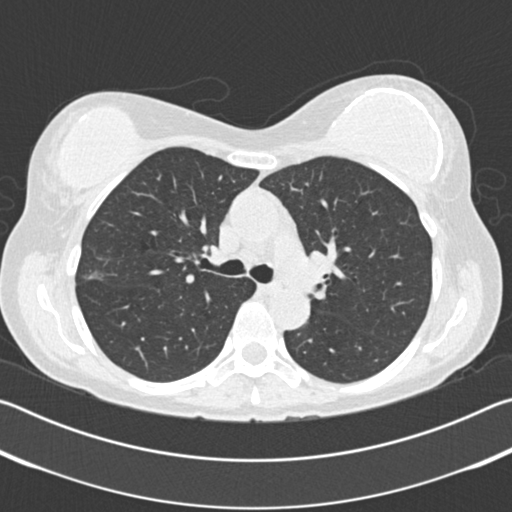
Chest CT (low-dose screening protocol), one axial image. Second annual screen. Lung window (W 1500 / L -600 HU). 2 mm slice thickness. Standard (soft-tissue) reconstruction kernel (B30f). 120 kVp. Slice 63 of 183 in the series. Female, age 58 years at enrolment. Former smoker at enrolment.
Expert-annotated lung lesion, bounding box (x1, y1, x2, y2) in pixels: (61, 256, 119, 301). The exam's reader record, not a measurement of the box and not confirmed to be the same lesion: non-calcified nodule or mass ≥4 mm, right upper lobe, 15 × 13 mm, poorly defined margins, ground glass attenuation, pre-existing on the prior screen: no. Participant outcome: lung cancer diagnosed 120 days after this screen — bronchiolo-alveolar adenocarcinoma, NOS, right upper lobe, well differentiated (G1), stage IA (AJCC 6th edition).